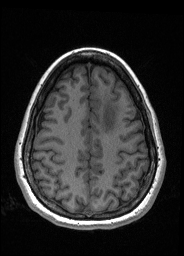
Pre-operative brain MRI before brain-tumour surgery, one axial slice; slice 58 of 176 in the series (ordered by position); T1-weighted post-contrast; 184 × 256 image matrix, field of view 180 × 250 mm. From the clinical record (not read from this slice): histopathology: Oligodendroglioma; WHO grade: 2; IDH mutation: yes.
Outlined on this slice (expert manual segmentation):
- tumour: bounding box <100,96,118,133> (left, top, right, bottom; pixels)